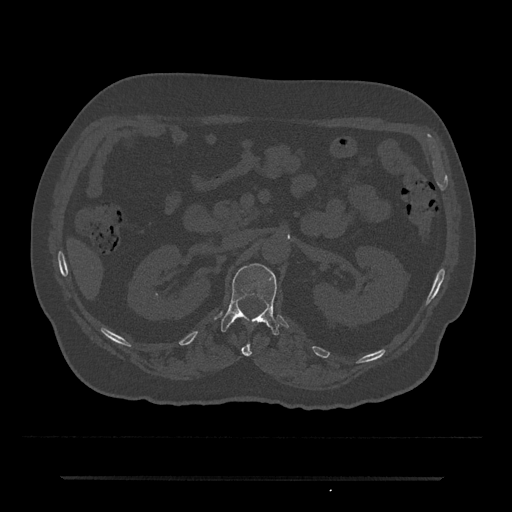
CT including the spine, one axial slice. Slice 81 of 797 in the series (ordered by position). 120 kVp. Bone window (W 1800 / L 400 HU). 512 × 512 image matrix, field of view 437 × 437 mm. Male patient, age 69 years. From the clinical record (not read from this slice): primary cancer: prostate.
Structures marked on this image (semi-automatic segmentation, software-assisted and operator-edited):
- L1 vertebra: bounding box [x1, y1, x2, y2] px = [221, 263, 279, 335]
- T12 vertebra: [241, 342, 252, 356]